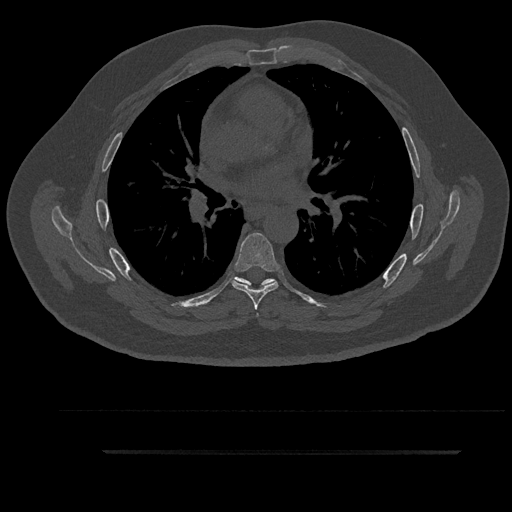
CT including the spine, one axial slice. Slice 568 of 797 in the series (ordered by position). Reconstruction kernel Br40s/3. 120 kVp. Bone window (W 1800 / L 400 HU). 0.5 mm slice thickness. 512 × 512 image matrix, field of view 432 × 432 mm. Patient: male, 63 years. From the clinical record (not read from this slice): primary cancer: renal.
Structures marked on this image (semi-automatic segmentation, software-assisted and operator-edited):
- T5 vertebra: bounding box <235,277,266,316> (left, top, right, bottom; pixels)
- T6 vertebra: <232,233,279,310>
- T7 vertebra: <239,278,276,286>